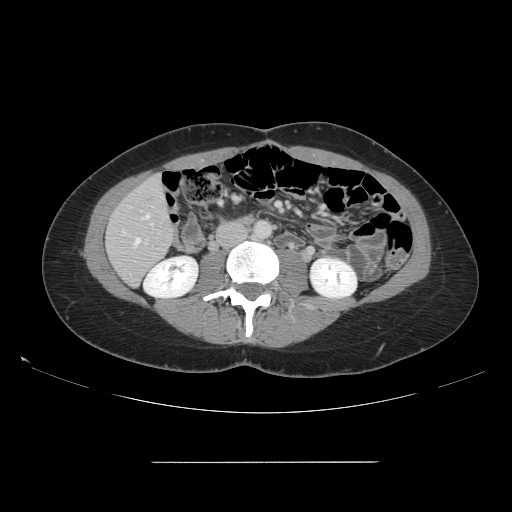
Contrast-enhanced abdominal CT, one axial slice. Slice 43 of 151 in the series (ordered by position). 120 kVp. Intravenous contrast given. Soft-tissue window (W 400 / L 40 HU). 2.5 mm slice thickness. 512 × 512 image matrix. Female patient, age 46 years. From the clinical record (not read from this slice): diagnosis: colorectal cancer liver metastases, imaged before liver resection; multiple liver metastases: yes; largest metastasis: 3 cm; disease in both lobes: yes.
Annotated regions visible in this slice (expert manual segmentation):
- hepatic veins: box from (x=135, y=214) to (x=149, y=245) px
- liver: (x=107, y=177)–(x=175, y=285)
- planned liver remnant (the part of the liver to remain after resection): (x=107, y=176)–(x=175, y=285)